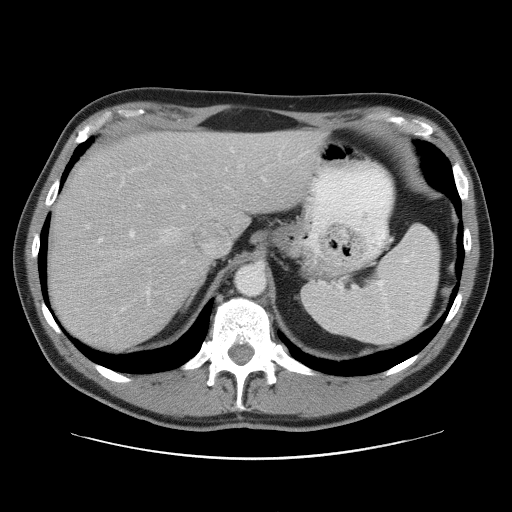
Contrast-enhanced abdominal CT, one axial slice. 120 kVp. Intravenous contrast given. Soft-tissue window (W 400 / L 40 HU). 5 mm slice thickness. 512 × 512 image matrix, field of view 393 × 393 mm. Male patient, age 70 years. Case-level facts recorded for this patient, not image findings: diagnosis: colorectal cancer liver metastases, imaged before liver resection; multiple liver metastases: yes; largest metastasis: 4 cm; chemotherapy before resection: yes.
Outlined on this slice (outlined manually by an expert reader):
- hepatic veins: box from (x=143, y=193) to (x=199, y=303) px
- liver: (x=47, y=132)–(x=321, y=351)
- planned liver remnant (the part of the liver to remain after resection): (x=110, y=132)–(x=321, y=221)
- portal vein (with intrahepatic branches): (x=129, y=148)–(x=233, y=238)